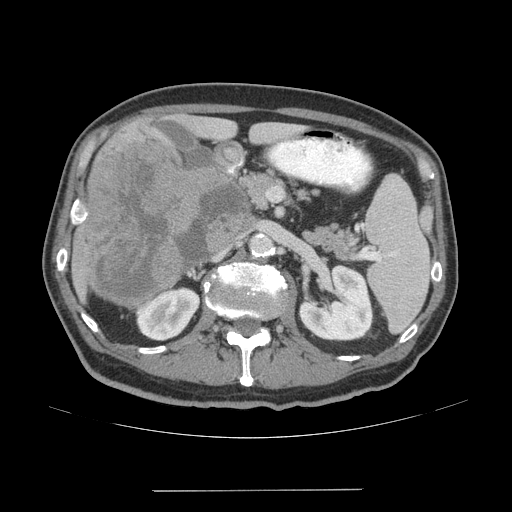
Contrast-enhanced abdominal CT (liver protocol), one axial slice; position 21 of 77 along the scan axis; reconstruction kernel STANDARD; soft-tissue window (W 400 / L 40 HU); 2.5 mm slice thickness; 512 × 512 image matrix, field of view 400 × 400 mm. Case-level facts recorded for this patient, not image findings: diagnosis: hepatocellular carcinoma (patient treated with transarterial chemoembolisation; whether this scan precedes or follows treatment is not stated here); TNM stage (as recorded): Stage-IVA; Child-Pugh class: A; tumour differentiation: well differentiated.
Outlined on this slice (semi-automatically segmented with operator editing):
- liver parenchyma outside the tumour (the mass and vessels are separate outlines, so this box may not span the whole liver): bounding box (x1, y1, x2, y2) in pixels: (72, 120, 300, 309)
- mass: (81, 138, 252, 307)
- liver vessels: (80, 212, 87, 222)